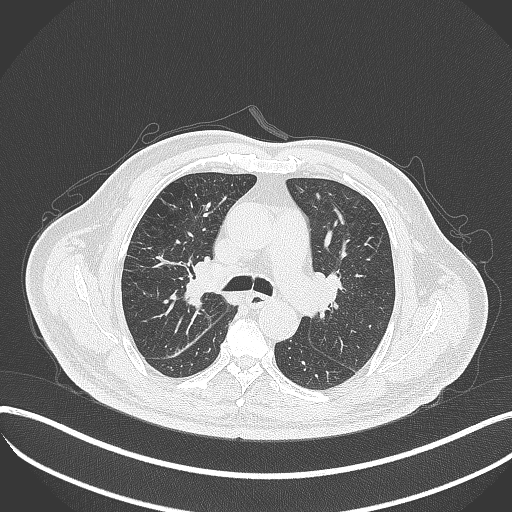
Chest CT, one axial slice; slice 234 of 401 in the series (ordered by position); reconstruction kernel B70f; lung window (W 1500 / L -600 HU); 1 mm slice thickness; 512 × 512 image matrix. Male patient, age 72 years. Case-level facts recorded for this patient, not image findings: clinical TNM (as recorded): T1c N0 M0; histopathological grade: G2.
Outlined on this slice (bounding box drawn by a radiologist):
- lung tumour (recorded histology: squamous cell carcinoma): bounding box <179,261,212,309> (left, top, right, bottom; pixels)